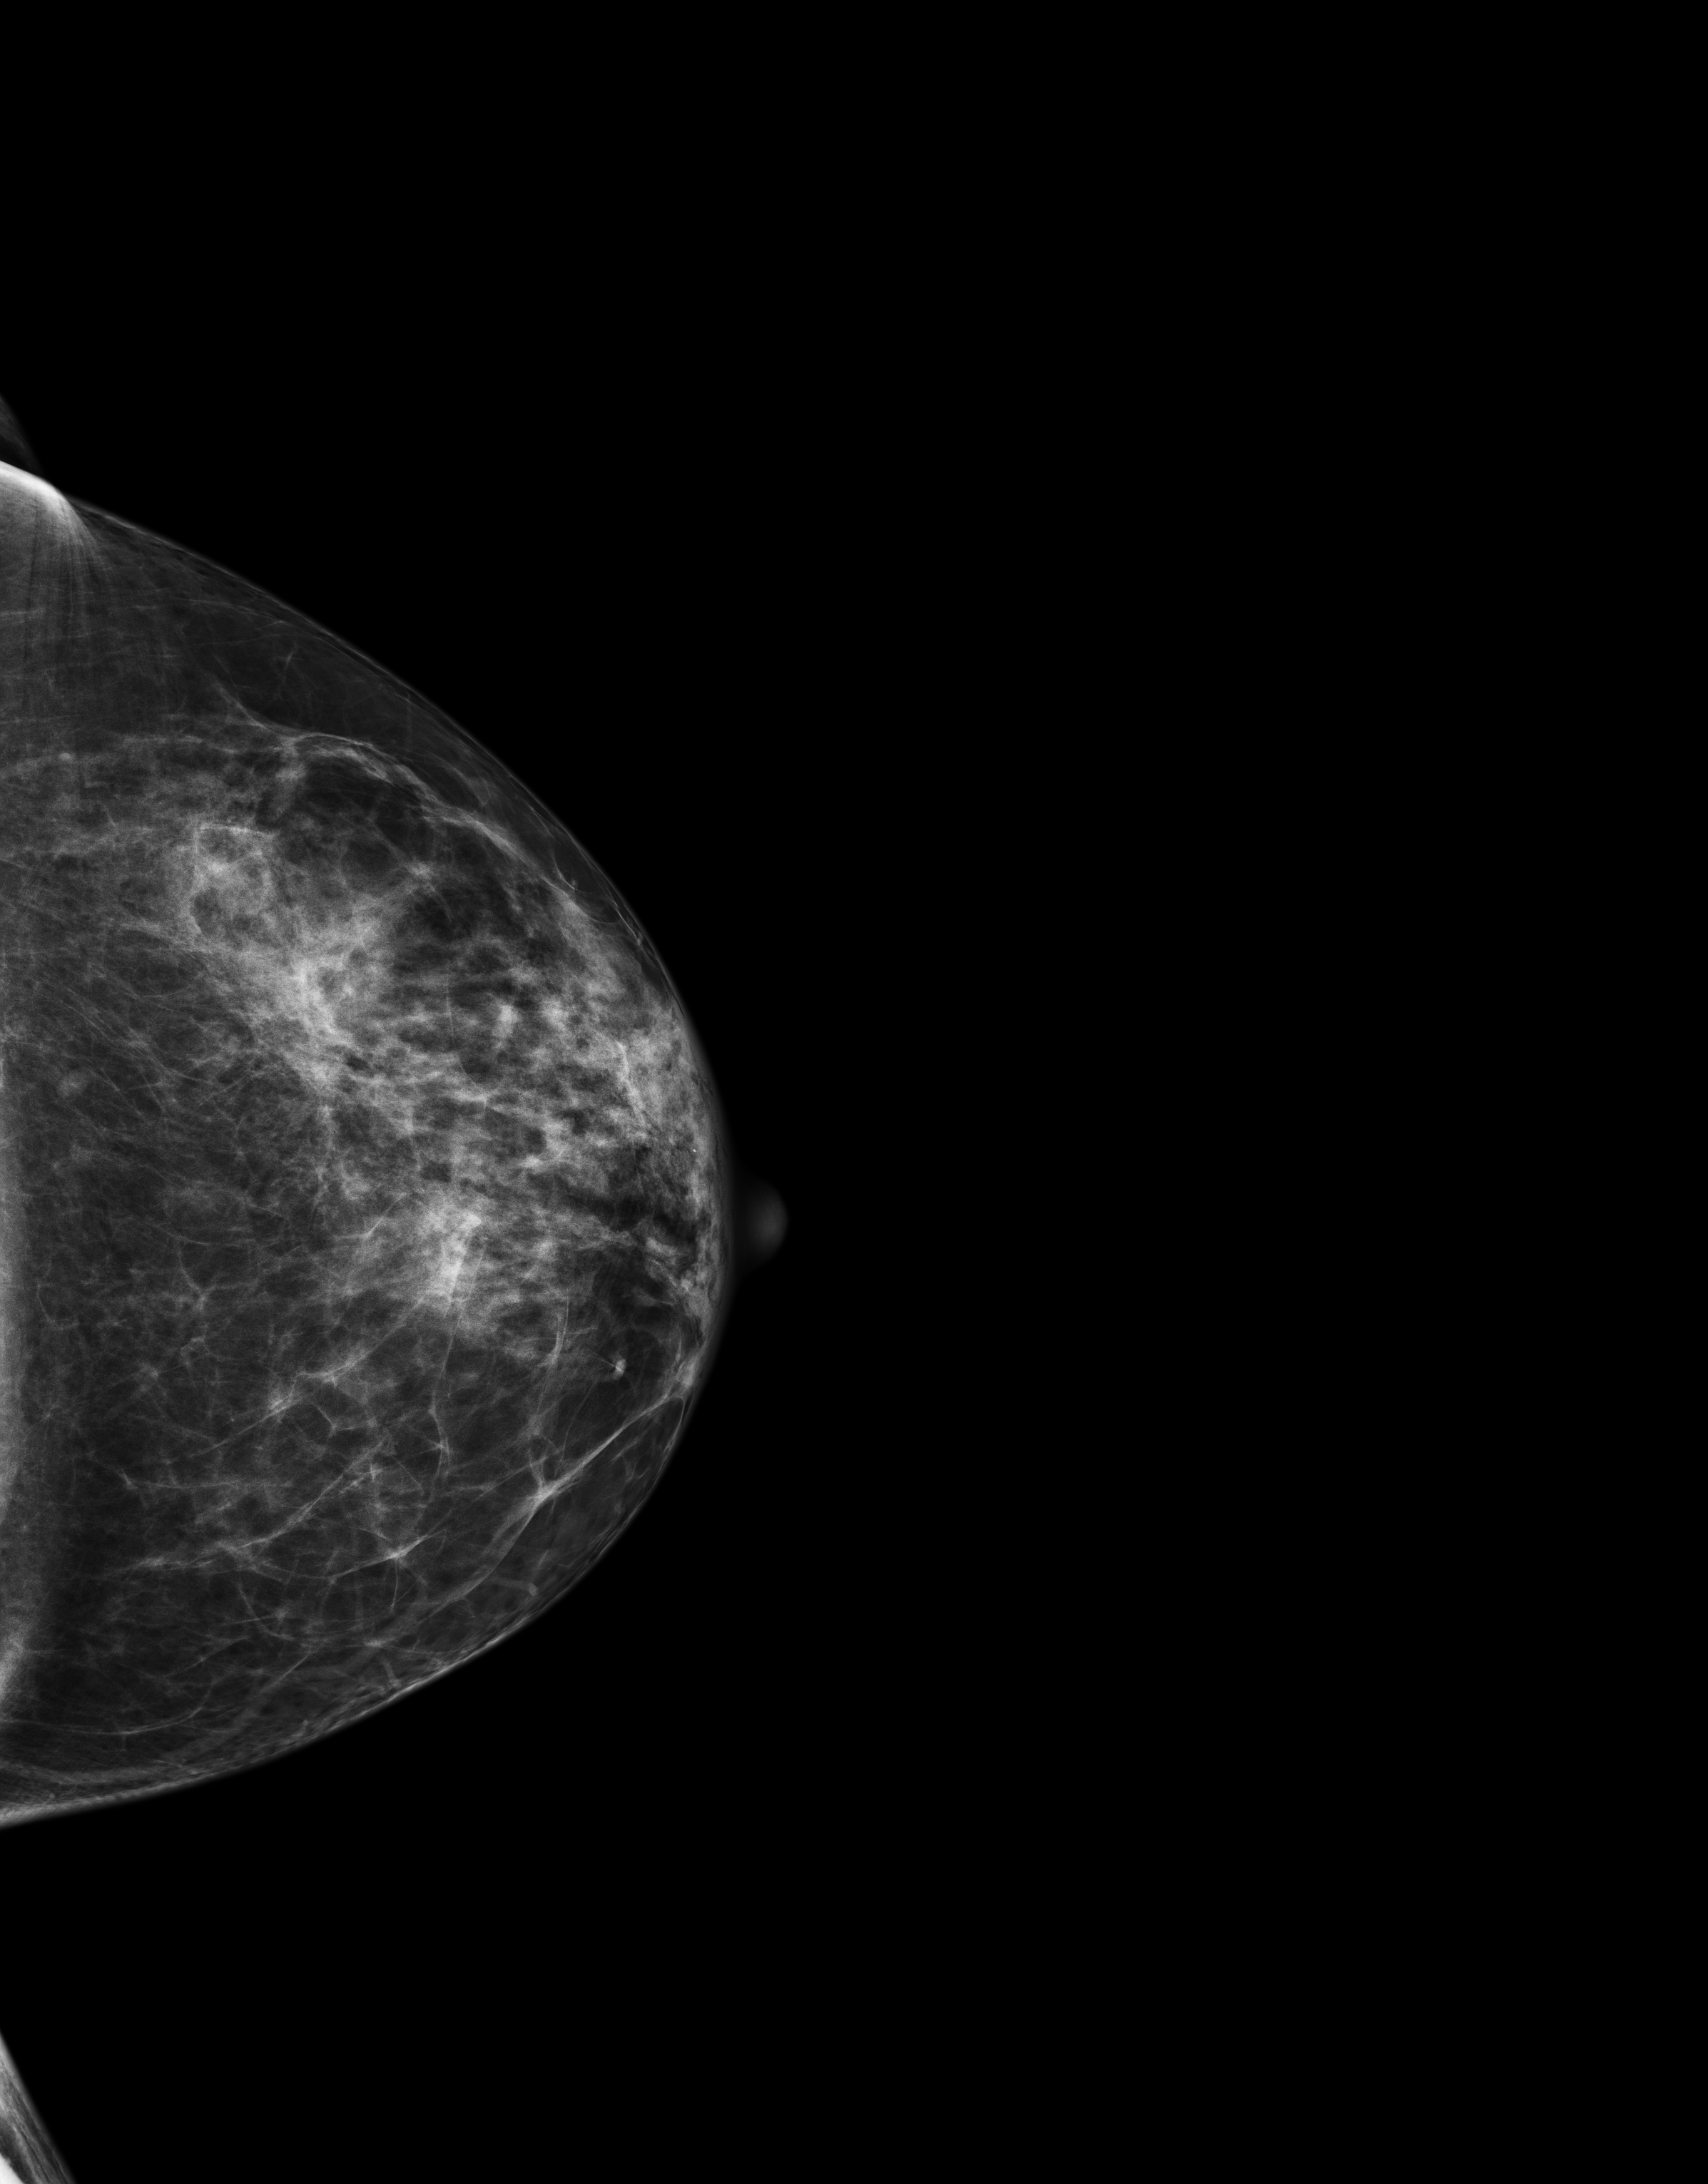
Full-field digital mammogram (FFDM); left breast; craniocaudal (CC) view; screening examination; compressed breast thickness 60 mm. Patient: female, 56 years.
Breast density at the screening exam (both breasts): heterogeneously dense (BI-RADS density category c). Final BI-RADS category for the screening round (tomosynthesis exam, both breasts): category 1. Recall: no recall after this screen.